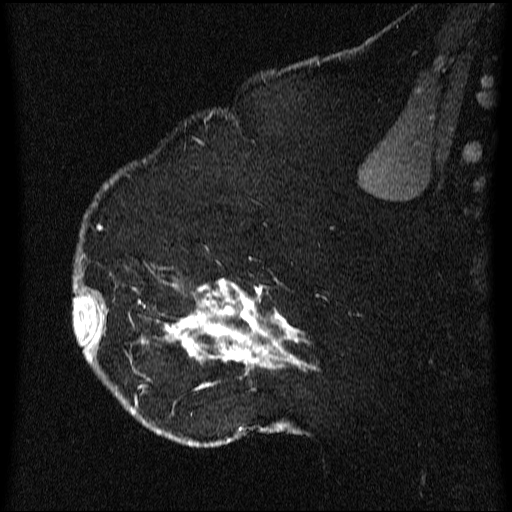
Breast MRI (dynamic contrast-enhanced), one sagittal slice; dynamic contrast-enhanced series, image 2 of 3 at this slice position (ordered by acquisition); 1.5 T; TE 4.2 ms, TR 9.1 ms; 2.2 mm slice thickness; 512 × 512 image matrix, field of view 180 × 180 mm. Patient: female, 52 years.
Structures marked on this image (semi-automatically segmented with operator editing):
- analysis volume of interest (the breast-tissue region the enhancement analysis was run in; not a lesion): box from (x=74, y=203) to (x=321, y=438) px
- tumour enhancement mask (voxels above the 70 % enhancement threshold inside the analysis volume of interest): (x=74, y=255)–(x=317, y=435)